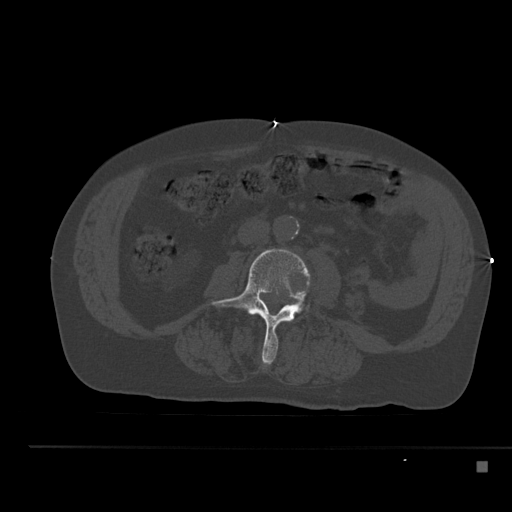
CT including the spine, one axial slice. Position 163 of 517 along the scan axis. Reconstruction kernel Br40s. 120 kVp. Bone window (W 1800 / L 400 HU). 1.5 mm slice thickness. 512 × 512 image matrix, field of view 408 × 408 mm. Patient: male, 70 years. Case-level facts recorded for this patient, not image findings: primary cancer: renal; vertebrae with lytic lesions (as recorded): T4, T6, T10, T12, L3, L4, L5.
Outlined on this slice (semi-automatically segmented with operator editing):
- L3 vertebra: bounding box (x1, y1, x2, y2) in pixels: (211, 249, 310, 364)